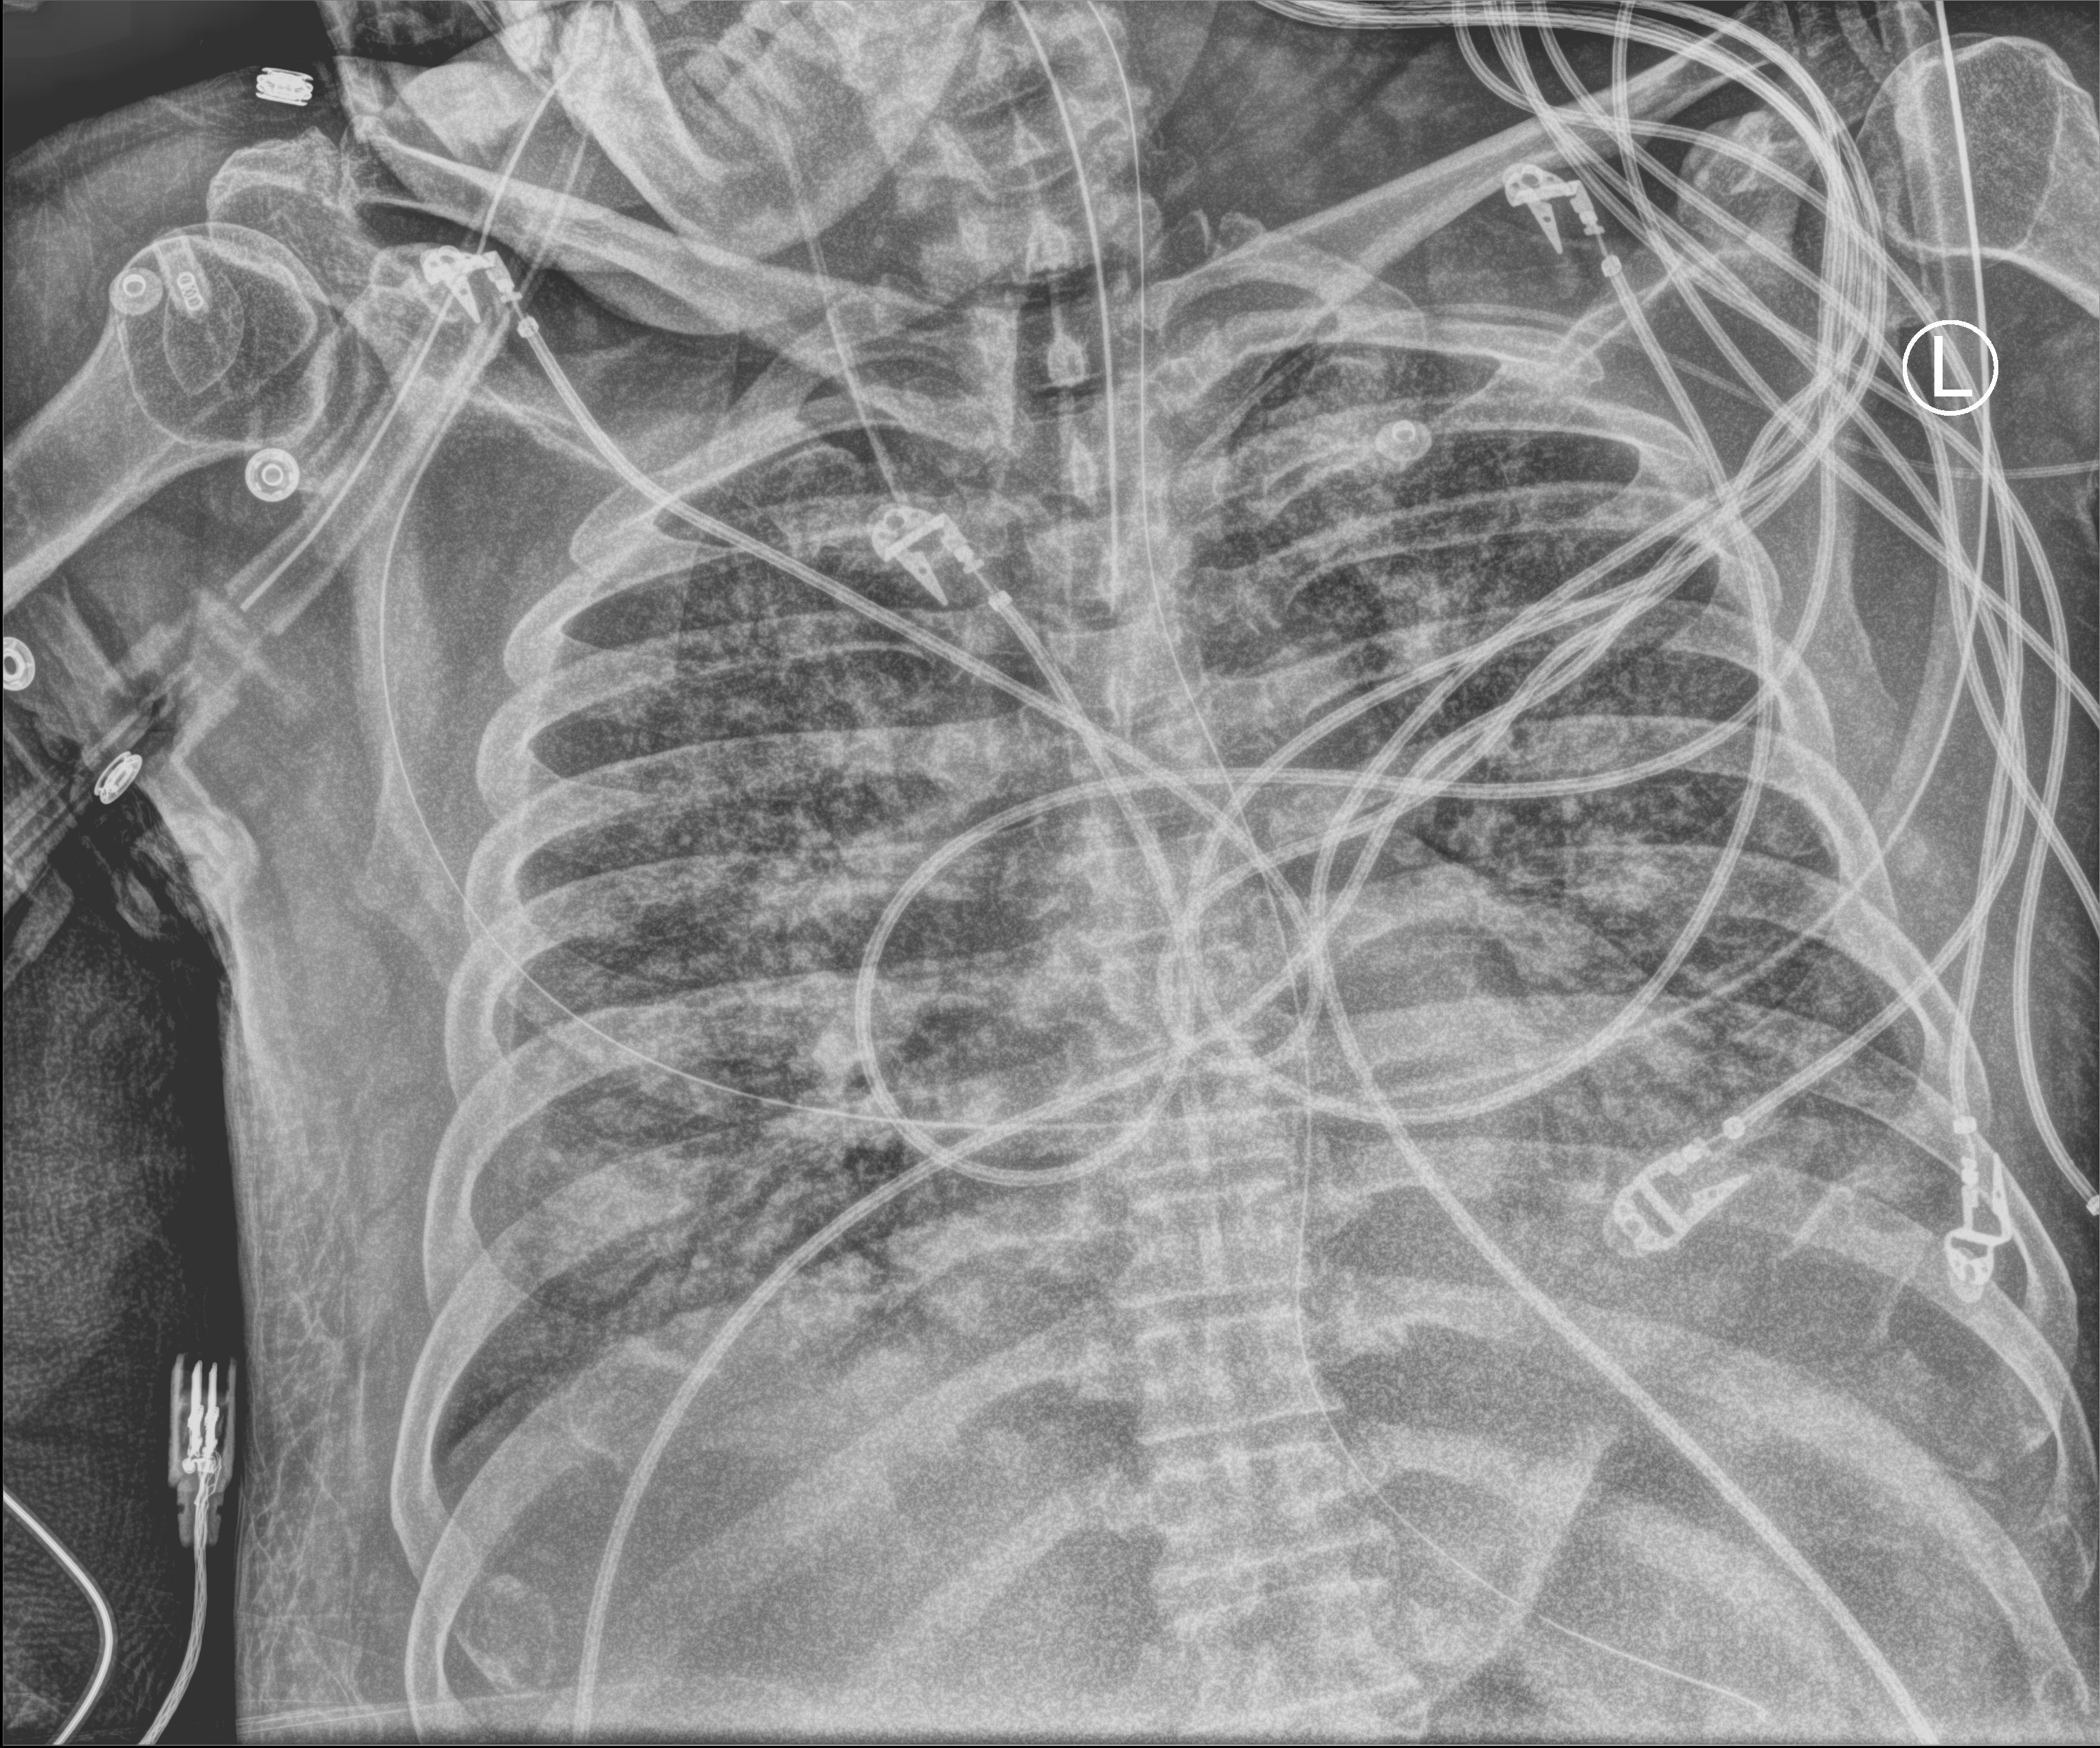
Bedside chest radiograph (computed radiography); anteroposterior (AP) projection. Male patient hospitalised with COVID-19, age 60–74 years.
From the hospital-stay record, not from the radiograph (when in the stay this image was taken is not recorded):
- mechanically ventilated during this hospital stay: yes
- admitted to intensive care during this hospital stay: yes
- COPD (admission record): no